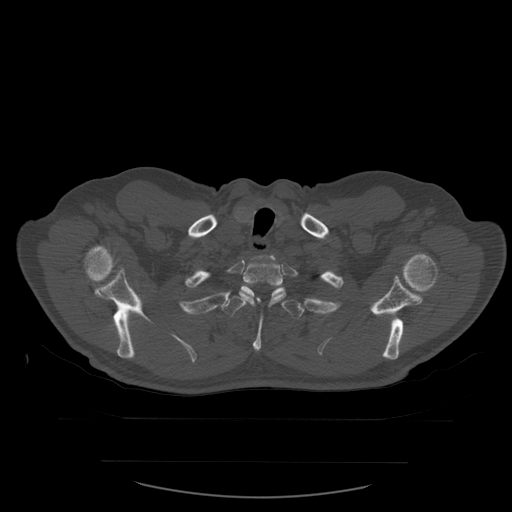
CT including the spine, one axial slice; slice 469 of 590 in the series (ordered by position); bone window (W 1800 / L 400 HU); 1.25 mm slice thickness; 512 × 512 image matrix. Patient age 71 years. Case-level facts recorded for this patient, not image findings: primary cancer: lung; vertebrae with lytic lesions (as recorded): T1, T2, L5, S1.
Annotated regions visible in this slice (semi-automatic segmentation, software-assisted and operator-edited):
- T1 vertebra: box from (x=254, y=255) to (x=276, y=261) px
- T2 vertebra: (x=240, y=260)–(x=286, y=304)
- T3 vertebra: (x=221, y=288)–(x=305, y=352)